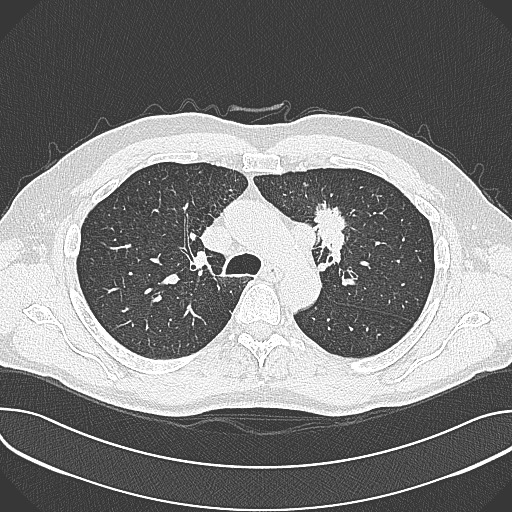
Chest CT (low-dose screening protocol), one axial image; first (baseline) screen; lung window (W 1500 / L -600 HU); lung (sharp) reconstruction kernel (B80f); 120 kVp; slice 102 of 361 in the series. Male participant, aged 59 years at enrolment. Current smoker at enrolment.
- Lesion marked by an expert reader, bounding box <302,197,361,257> (left, top, right, bottom; pixels).
- The screening reader recorded 2 non-calcified nodules or masses ≥4 mm on this exam (left upper lobe, left upper lobe); which of them this box marks is not recorded.
- Participant outcome: lung cancer diagnosed 21 days after this screen — non-small cell carcinoma, left upper lobe, poorly differentiated (G3), stage IIIA (AJCC 6th edition), 35 mm at pathology.